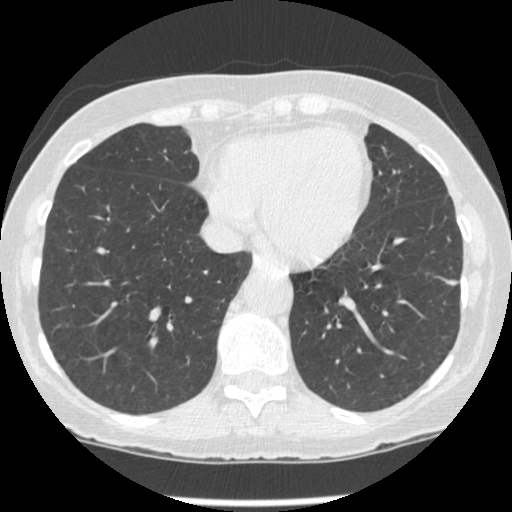
Low-dose screening chest CT, one axial slice; slice 77 of 247 in the series (ordered by position); 120 kVp; lung window (W 1500 / L -600 HU); 1.25 mm slice thickness; 512 × 512 image matrix, field of view 303 × 303 mm.
Outlined on this slice (outlined manually by an expert reader):
- lesion 1 (tumor, lower lobe of left lung): bounding box [x1, y1, x2, y2] px = [446, 280, 458, 286]